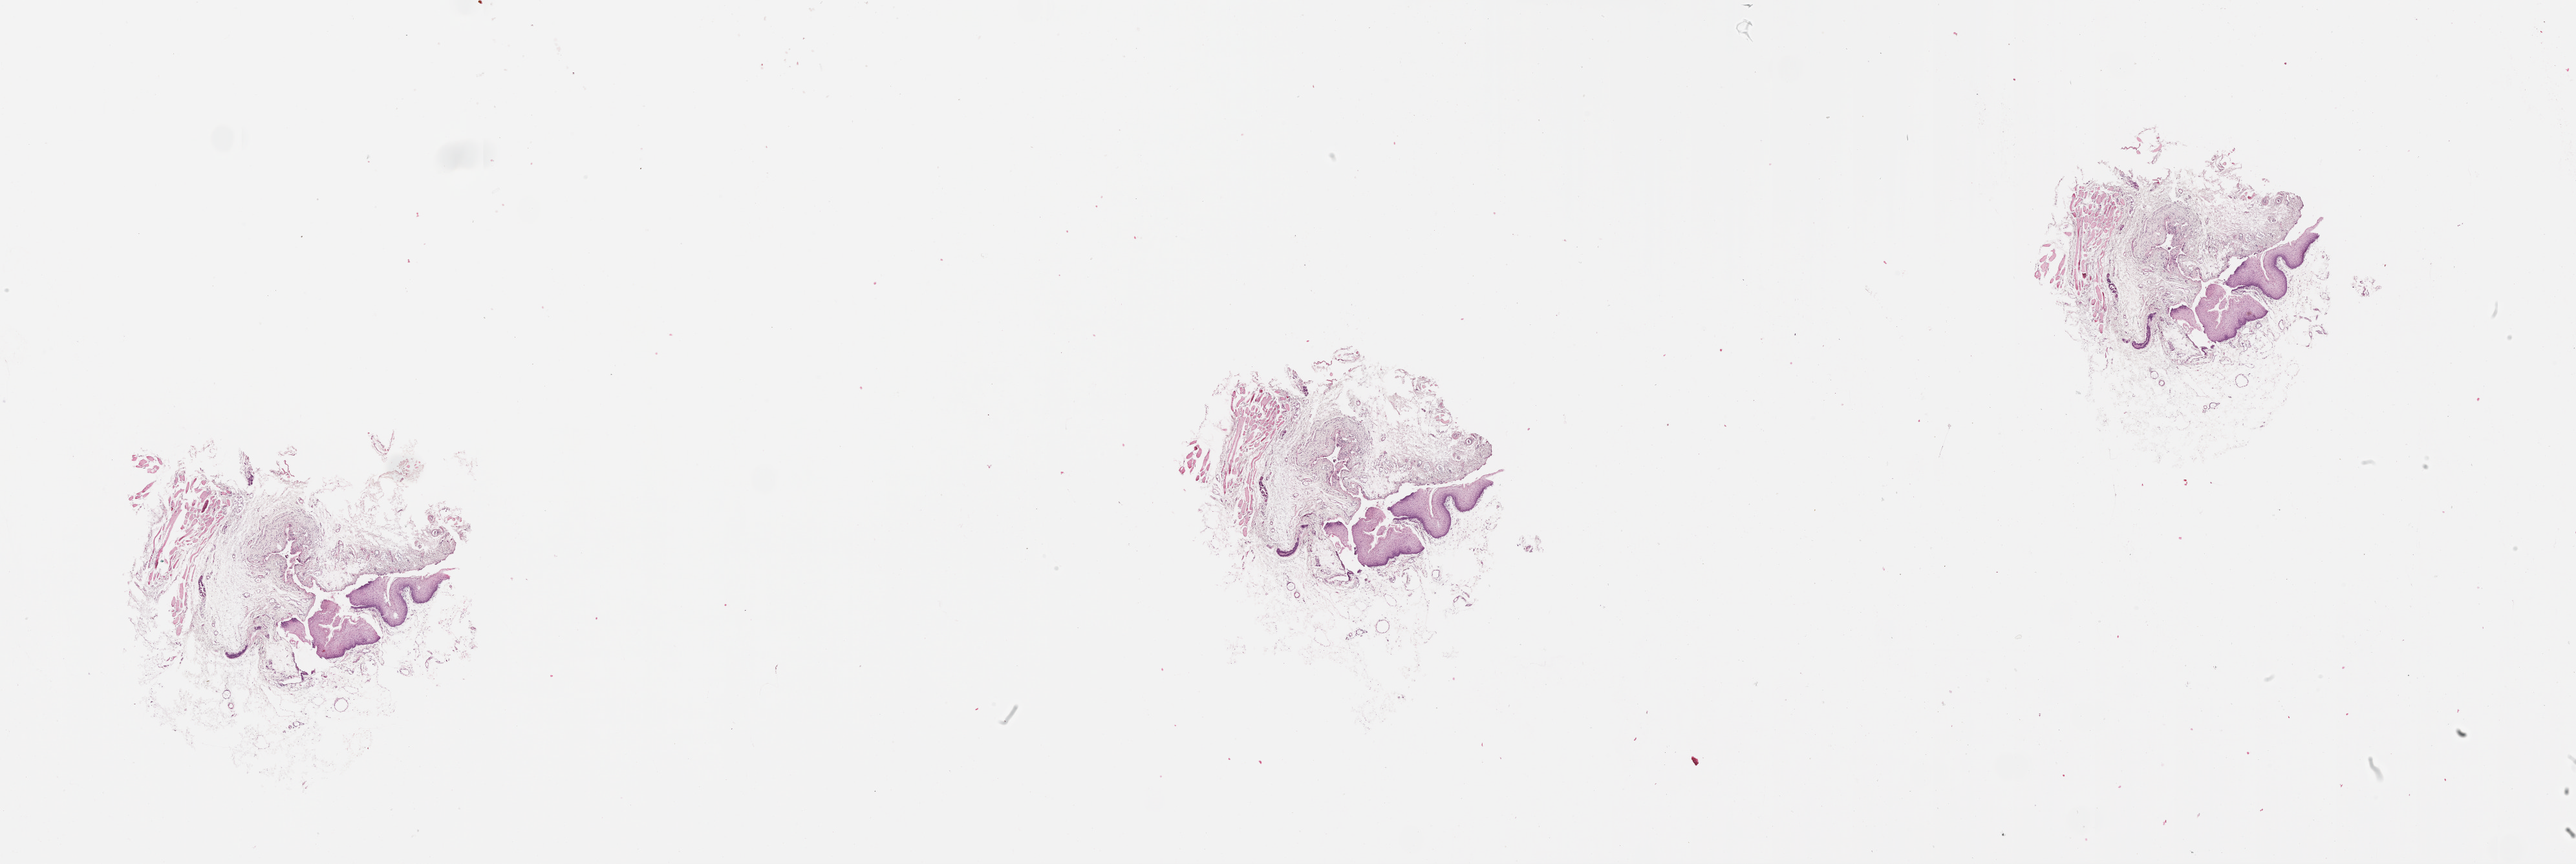
Digitized H&E-stained tissue section (whole slide), low-resolution overview of the scanned area, about 32.1 x 10.8 mm (from a 20x scan); head and neck, tissue type not recorded. Male, 76 y/o.
Patient diagnosis: Squamous cell carcinoma, NOS (tongue, NOS).